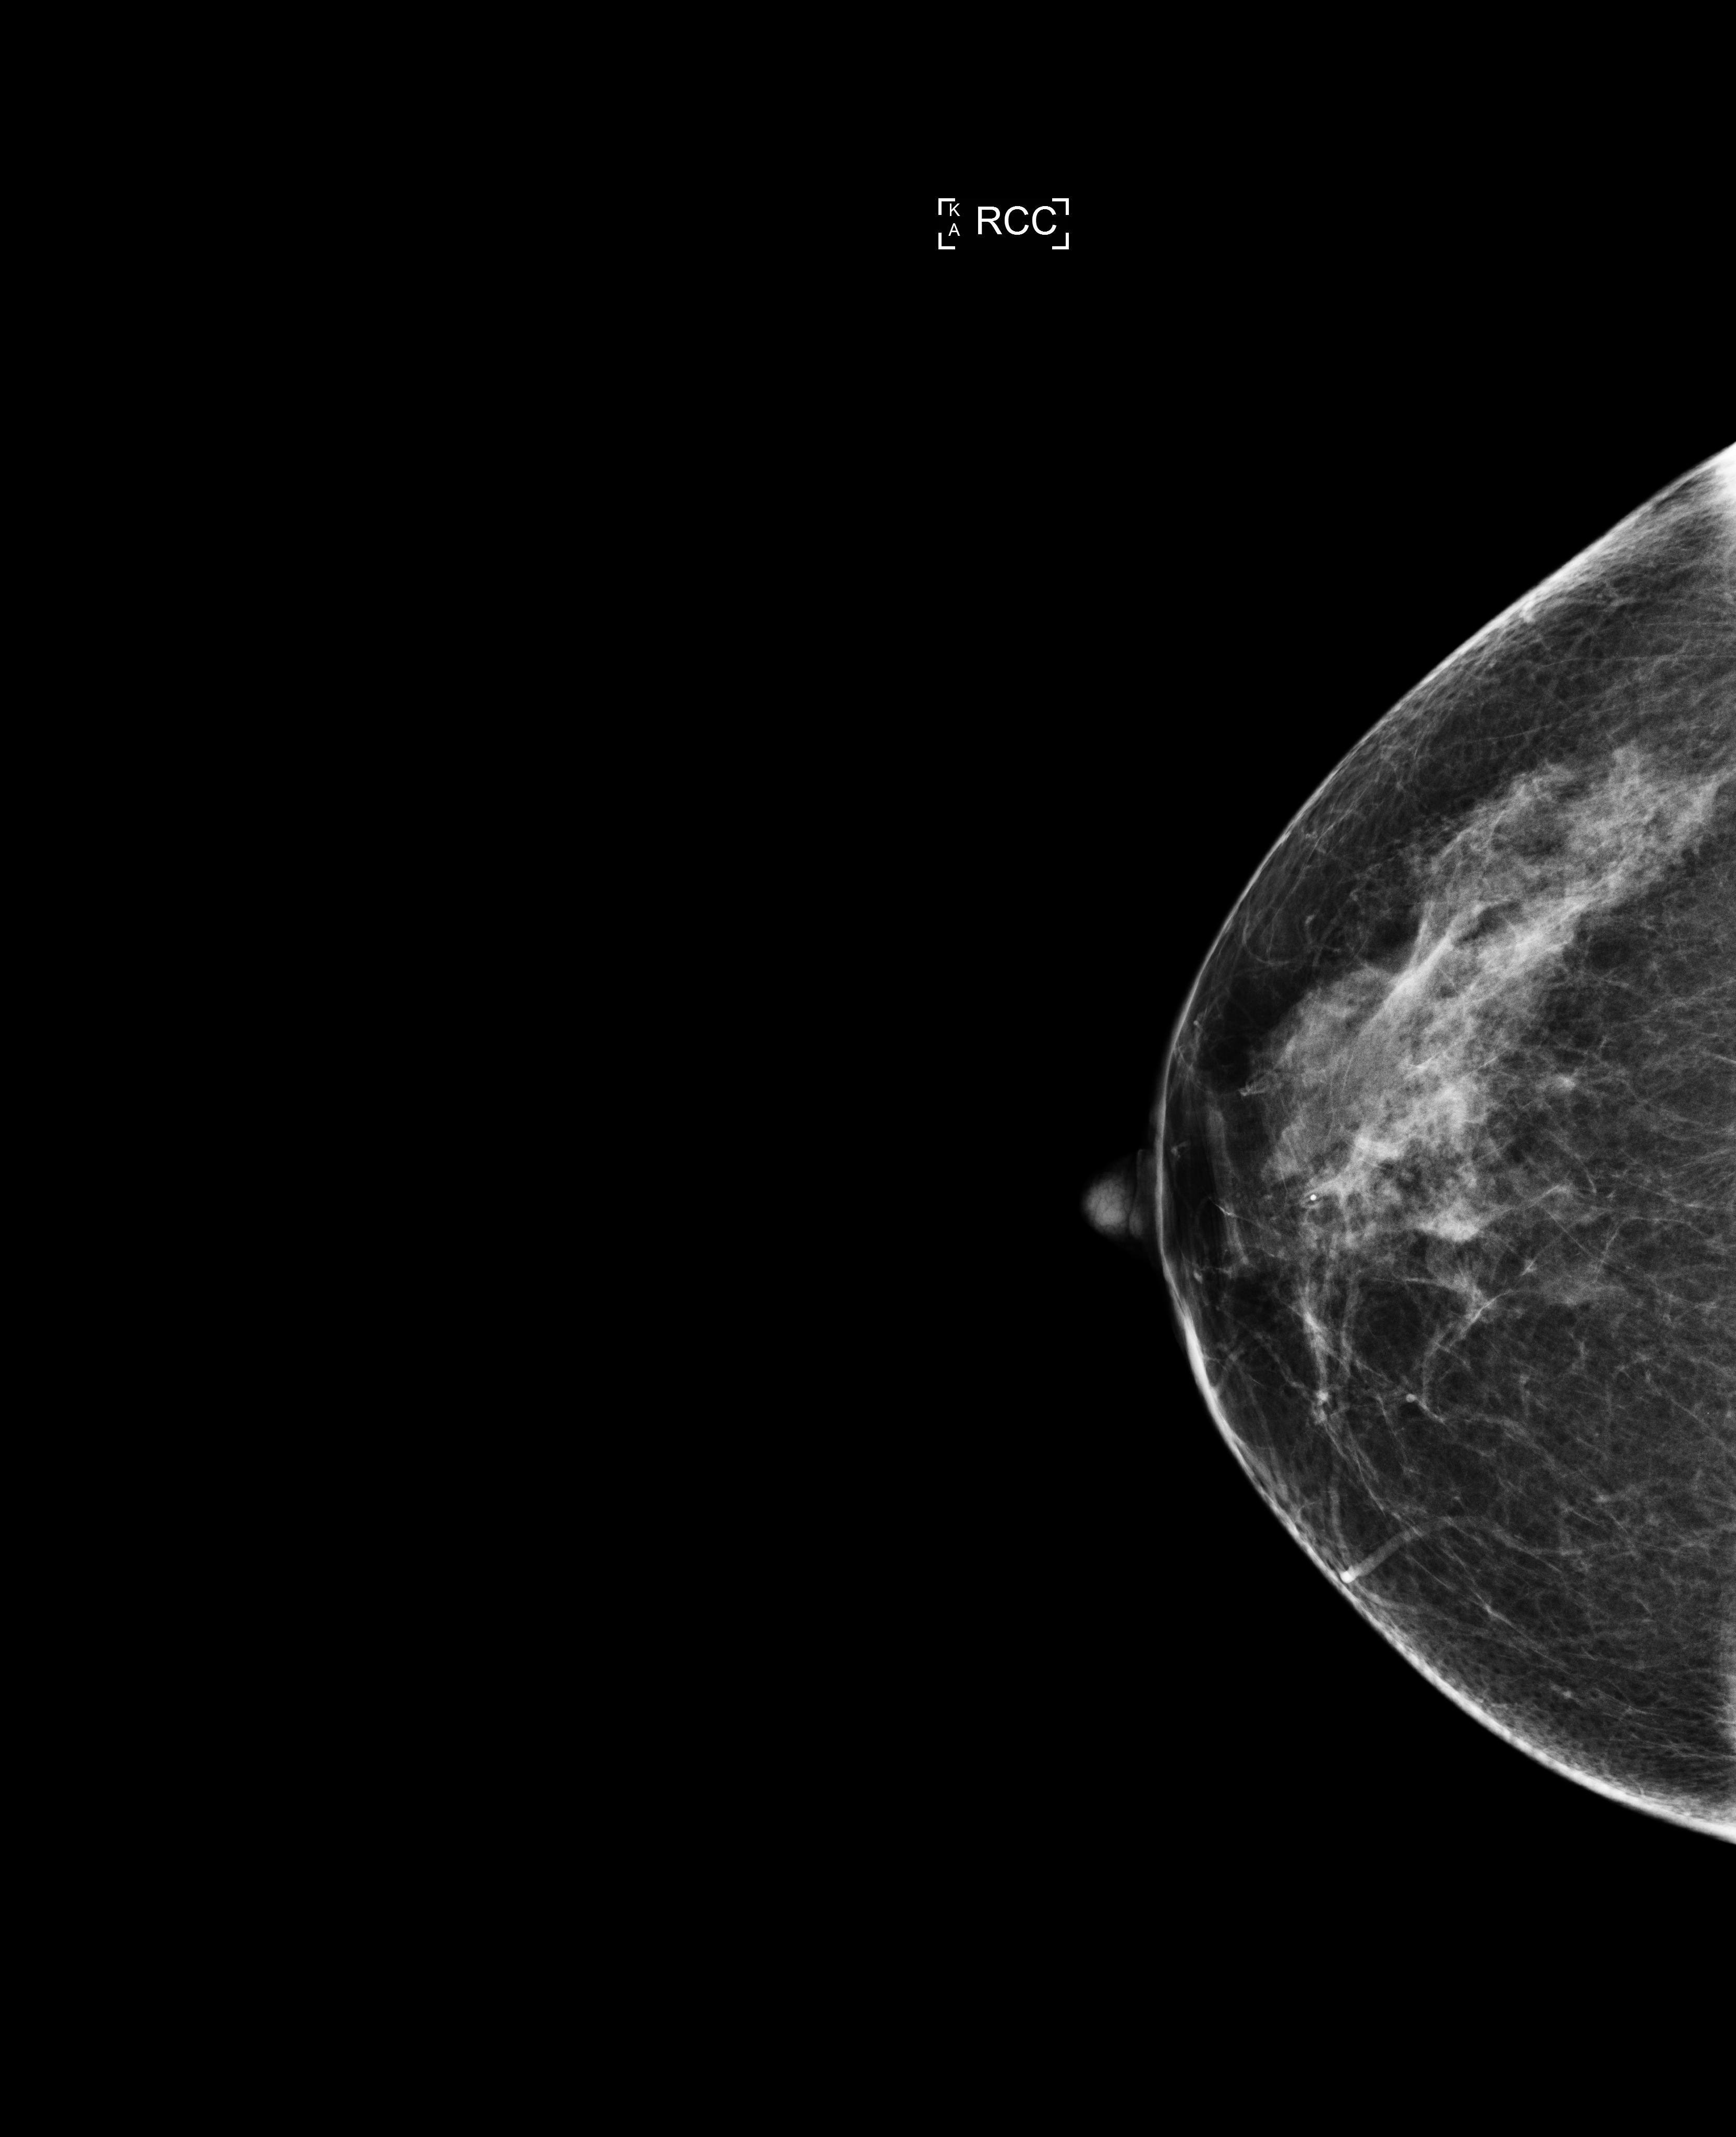
Annual screening mammography examination. Patient: female, 52 years.
Image type: full-field digital mammogram. Breast: right. Projection: craniocaudal (CC) view.